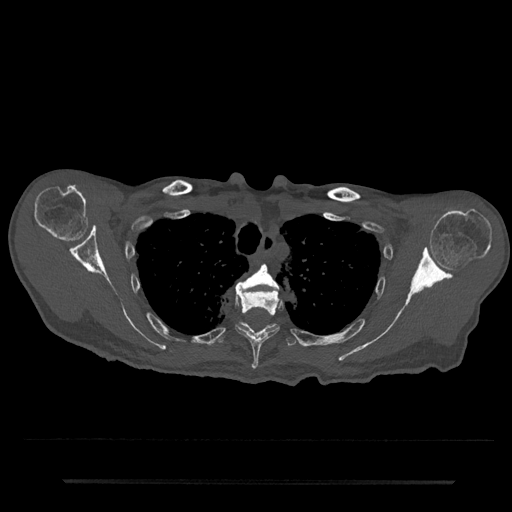
CT including the spine, one axial slice. Slice 618 of 797 in the series (ordered by position). 120 kVp. Bone window (W 1800 / L 400 HU). 0.5 mm slice thickness. 512 × 512 image matrix, field of view 427 × 427 mm. Male patient, age 74 years. Case-level facts recorded for this patient, not image findings: primary cancer: prostate.
Structures marked on this image (semi-automatically segmented with operator editing):
- T3 vertebra: bounding box [x1, y1, x2, y2] px = [236, 265, 279, 292]
- T4 vertebra: [235, 288, 281, 369]
- T5 vertebra: [217, 322, 297, 347]